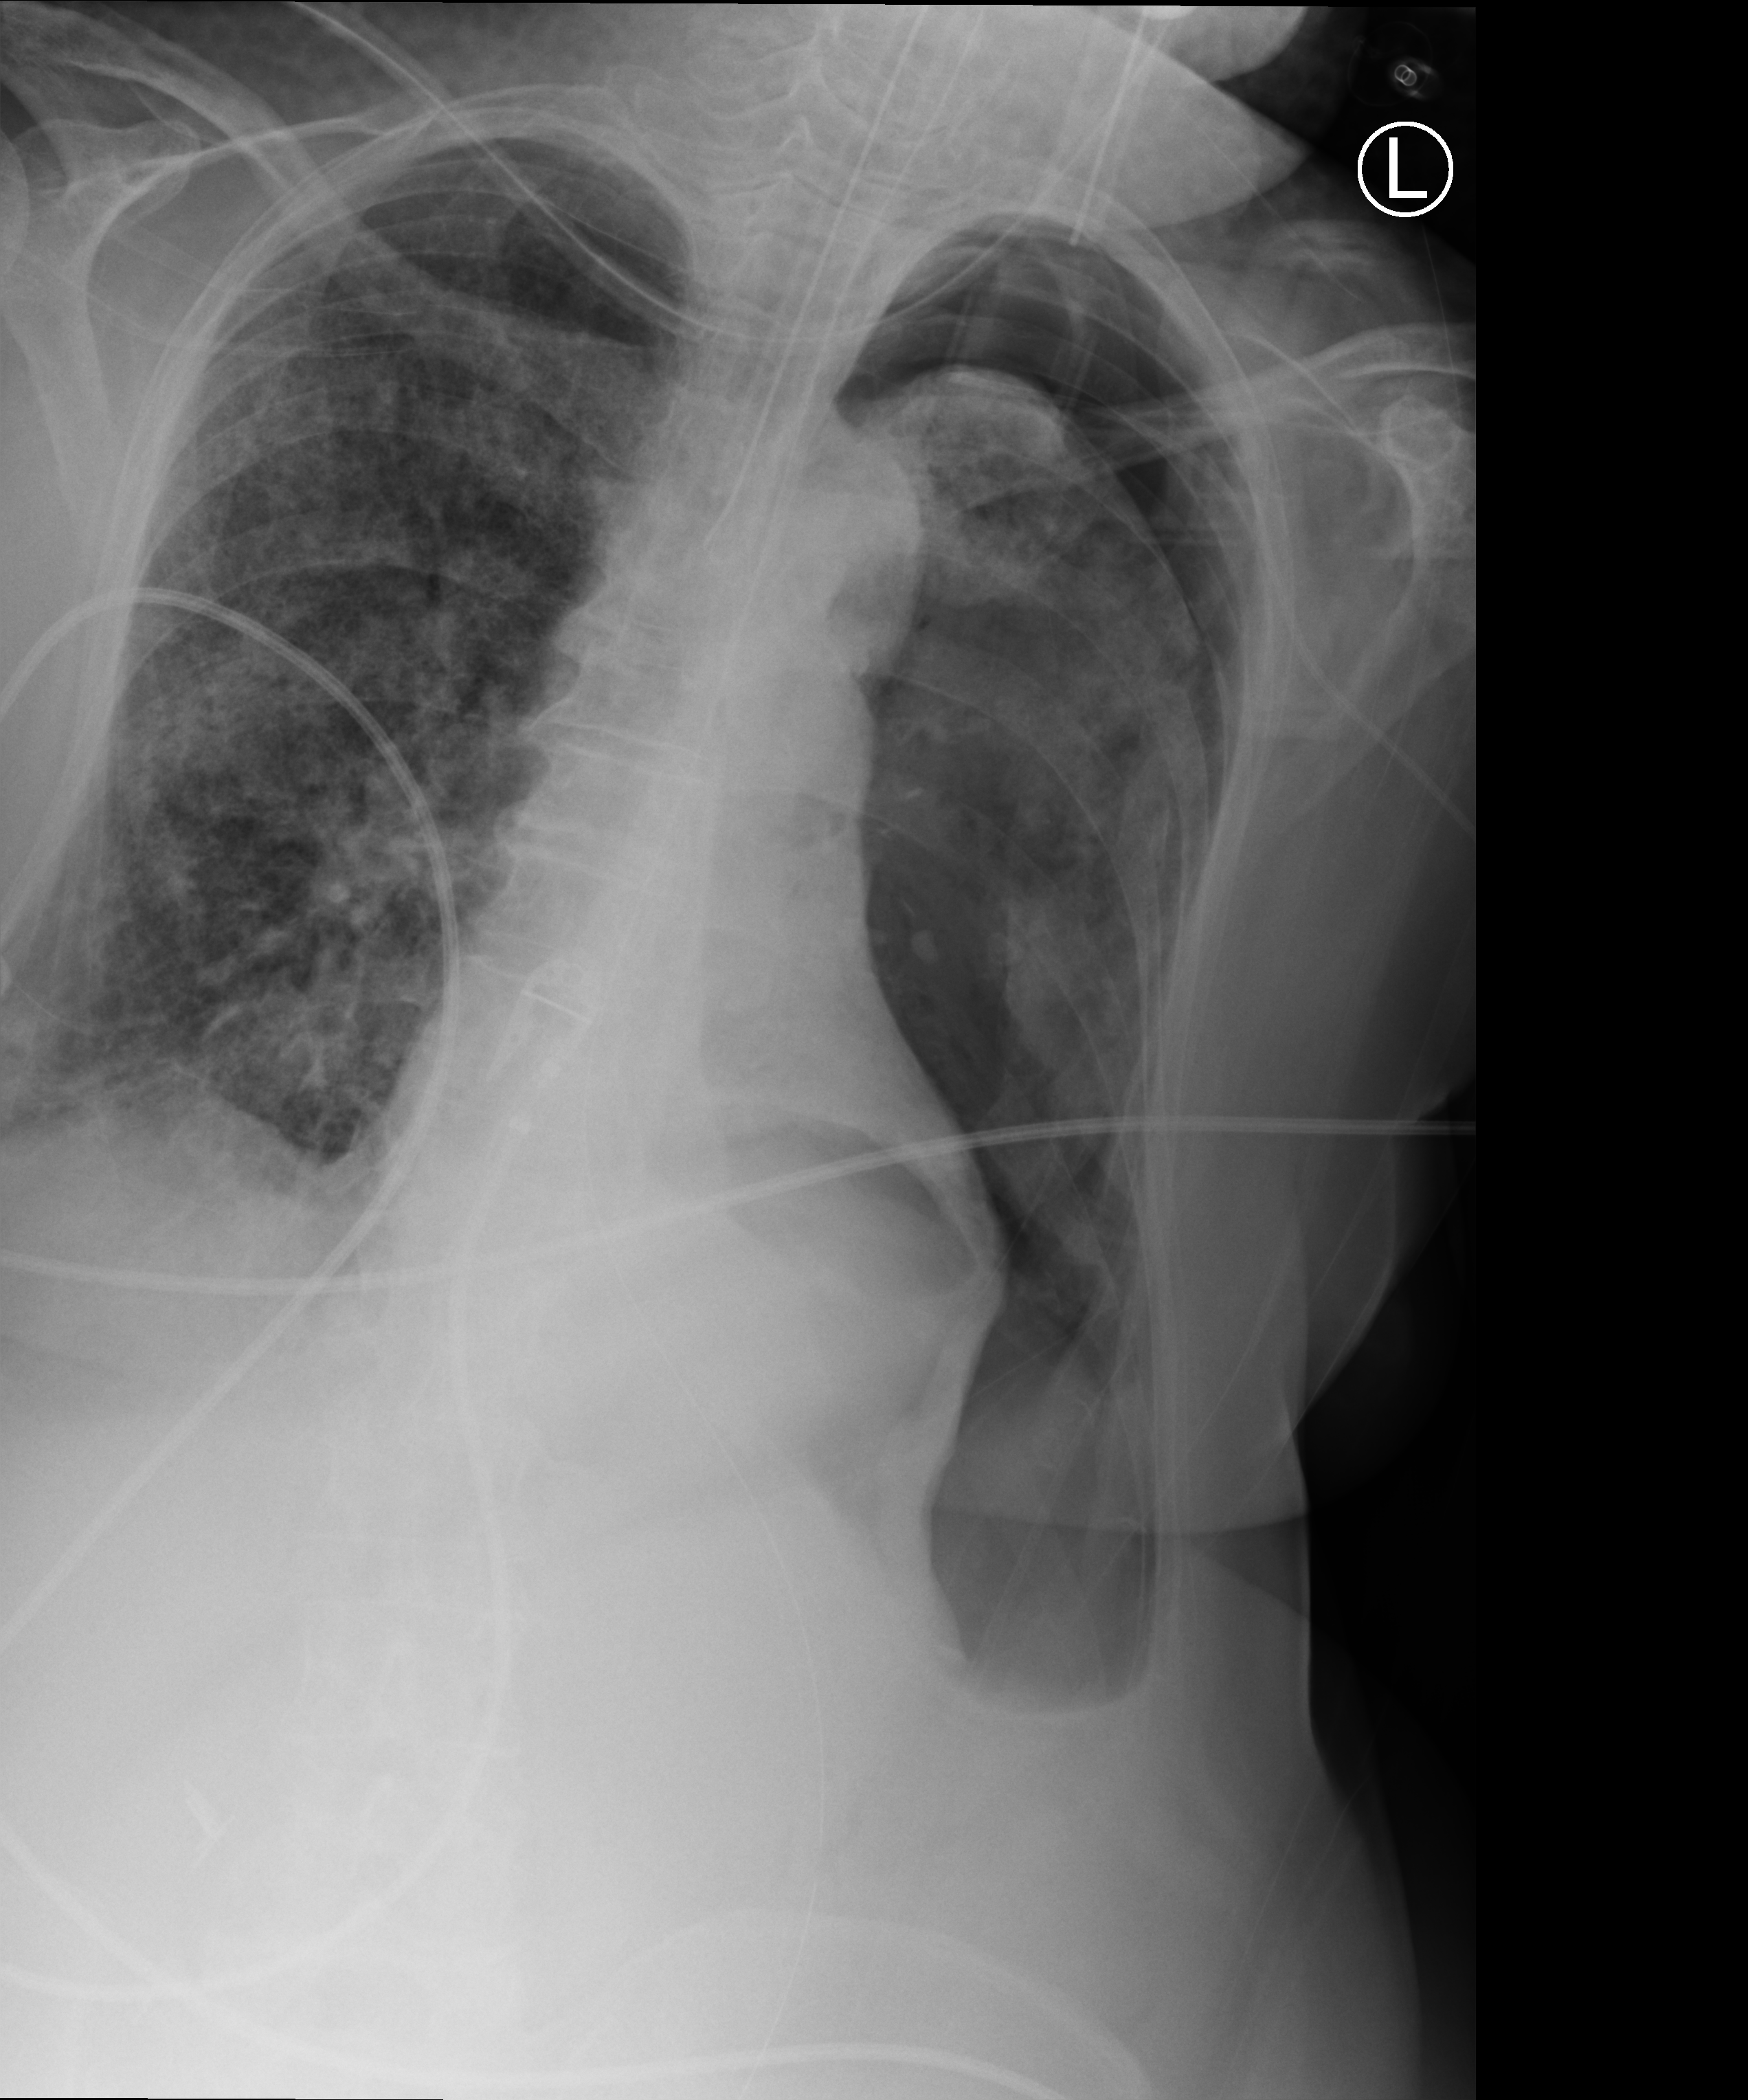
Portable chest radiograph; anteroposterior (AP) projection. Patient hospitalised with COVID-19; female, aged 75–90 years.
Admission-level facts for this patient (not findings on this image; timing relative to this image not recorded): COPD (admission record): no.